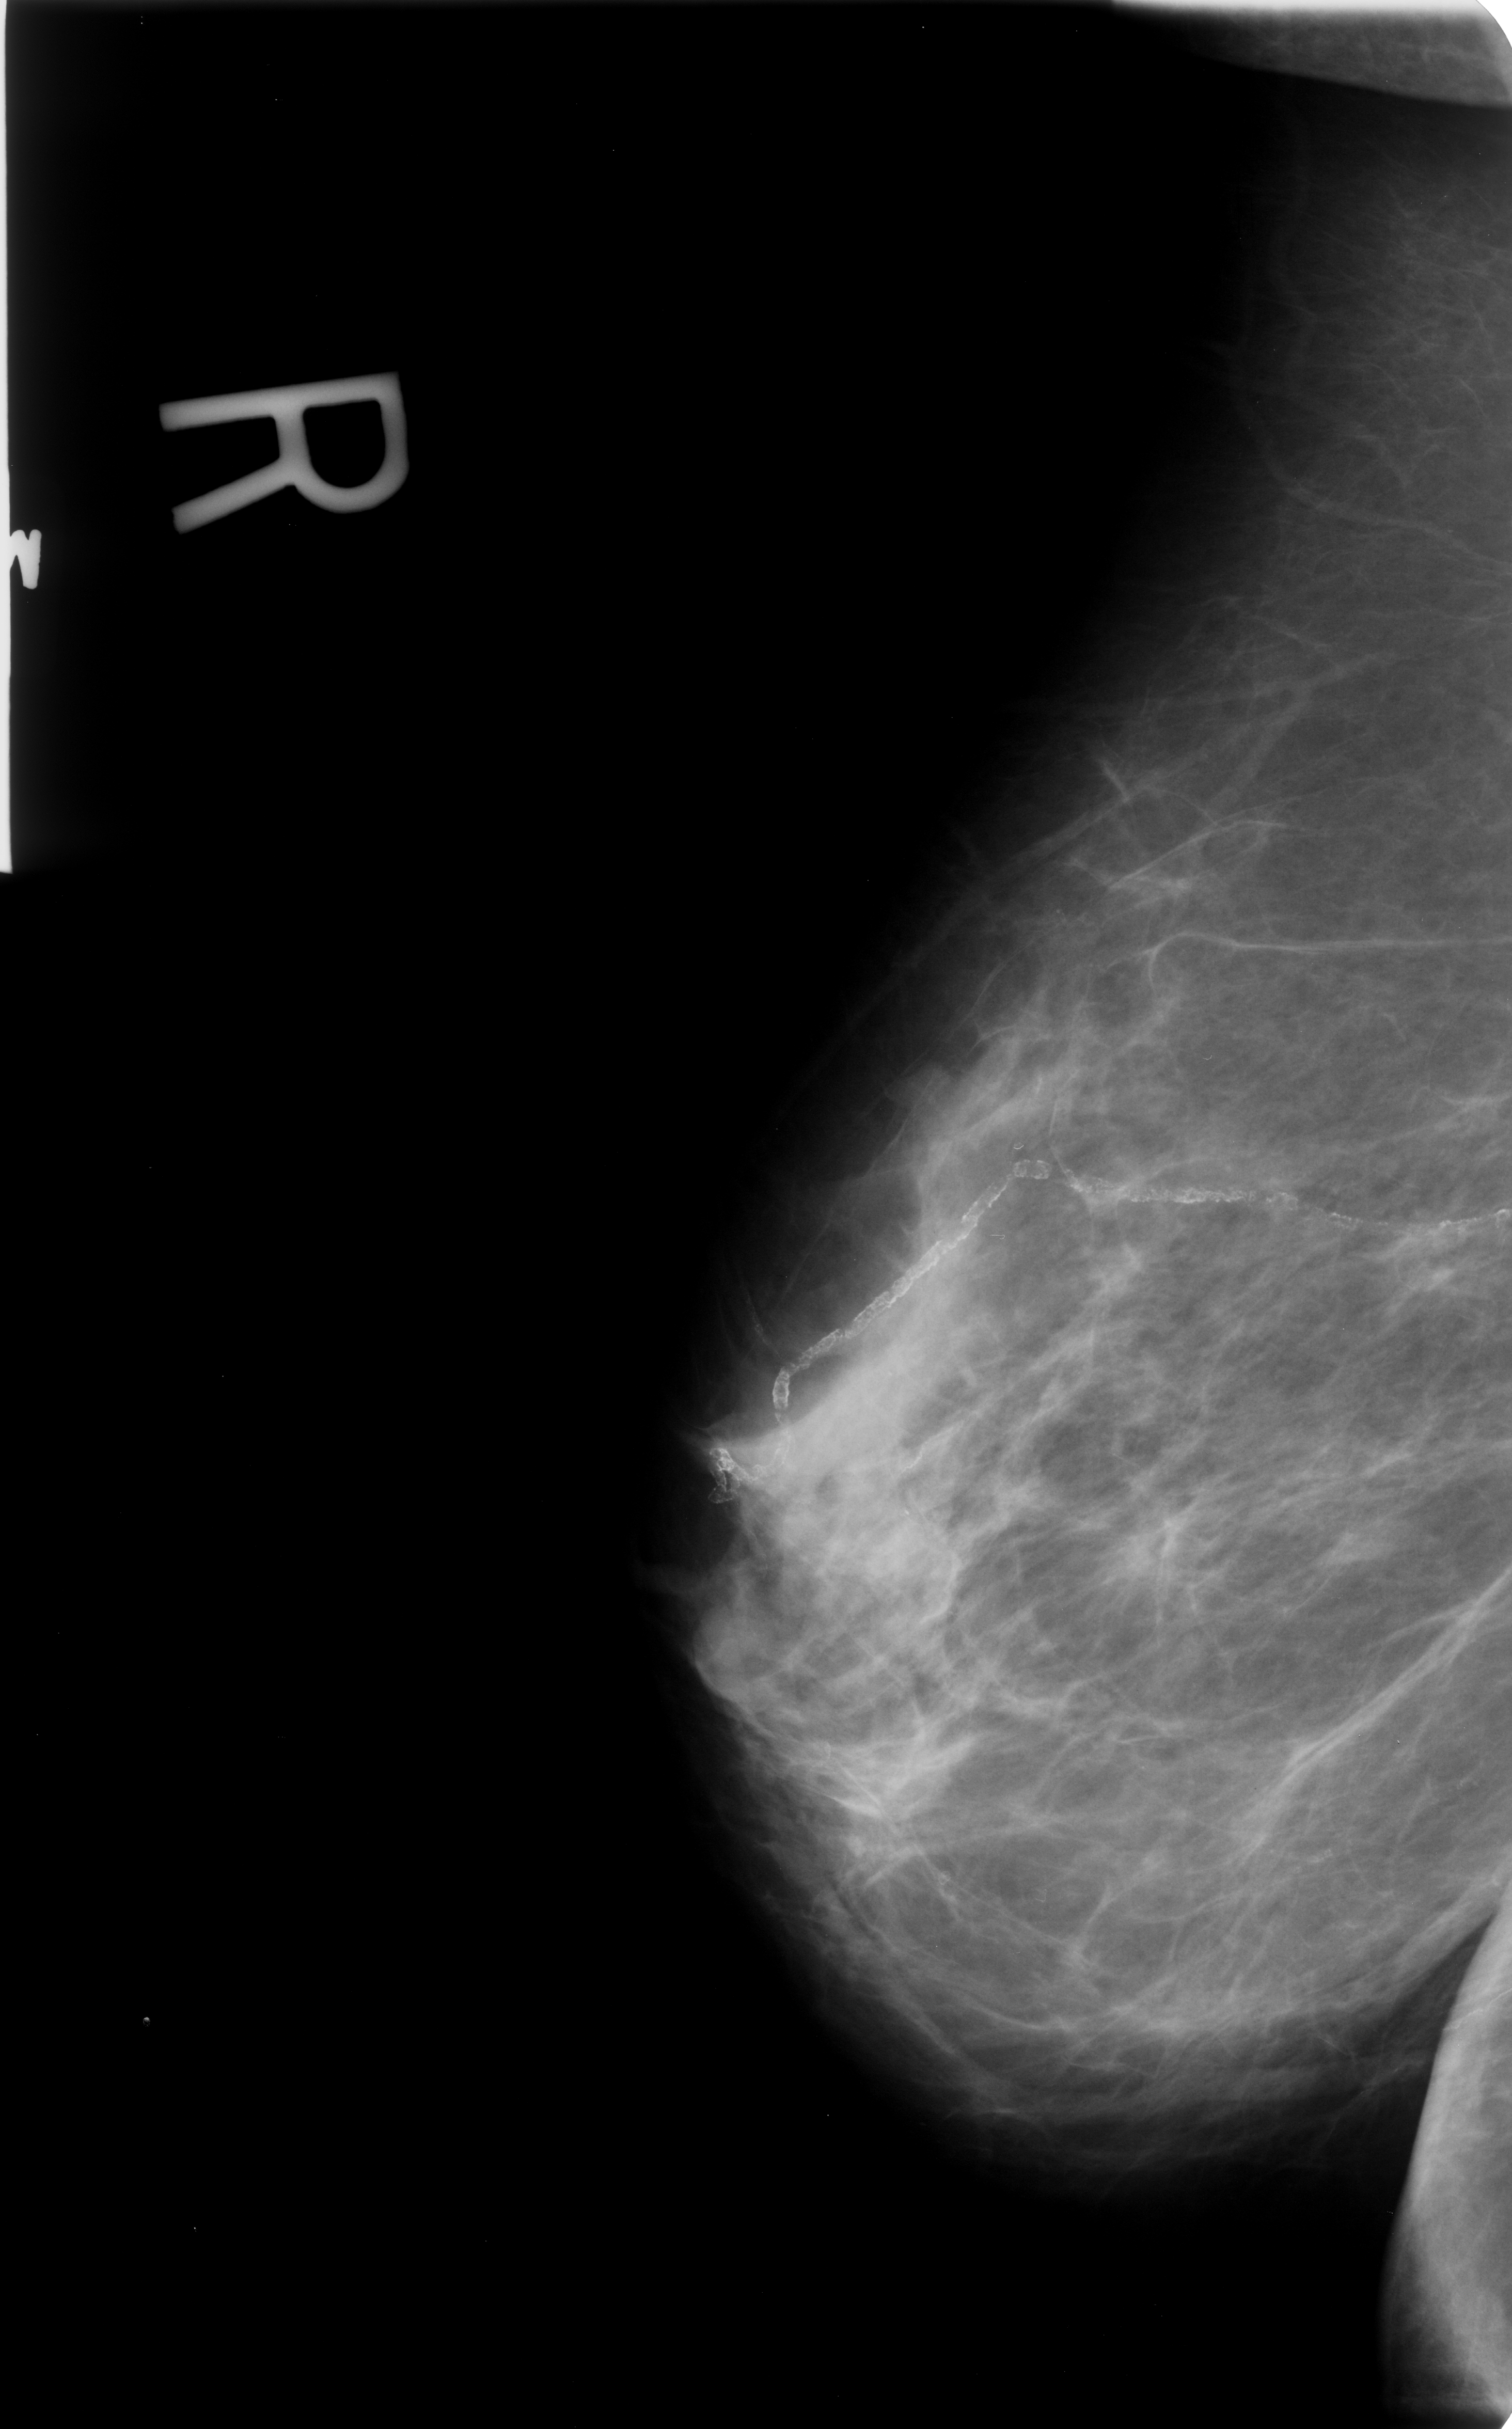
Scanned film-screen mammogram. Right breast. MLO view. BI-RADS breast density category 2 (scale 1–4). 1512 × 2429 image matrix.
Expert-marked regions of interest on this image (one box per marked abnormality):
- calcifications, morphology vascular; BI-RADS assessment category 2; outcome (as recorded, no biopsy): benign without callback (not worked up further): bounding box [x1, y1, x2, y2] px = [756, 1148, 1451, 1472]